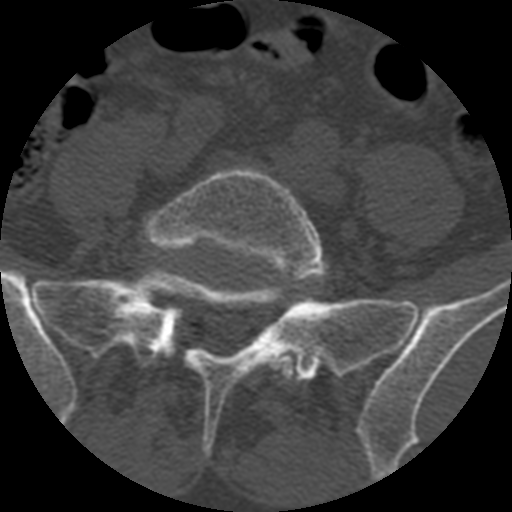
CT including the spine, one axial slice; position 245 of 399 along the scan axis; bone window (W 1800 / L 400 HU); 1.25 mm slice thickness; 512 × 512 image matrix, field of view 160 × 160 mm. Patient age 71 years. From the clinical record (not read from this slice): primary cancer: prostate.
Outlined on this slice (semi-automatic segmentation, software-assisted and operator-edited):
- L5 vertebra: bounding box [x1, y1, x2, y2] px = [145, 167, 327, 383]